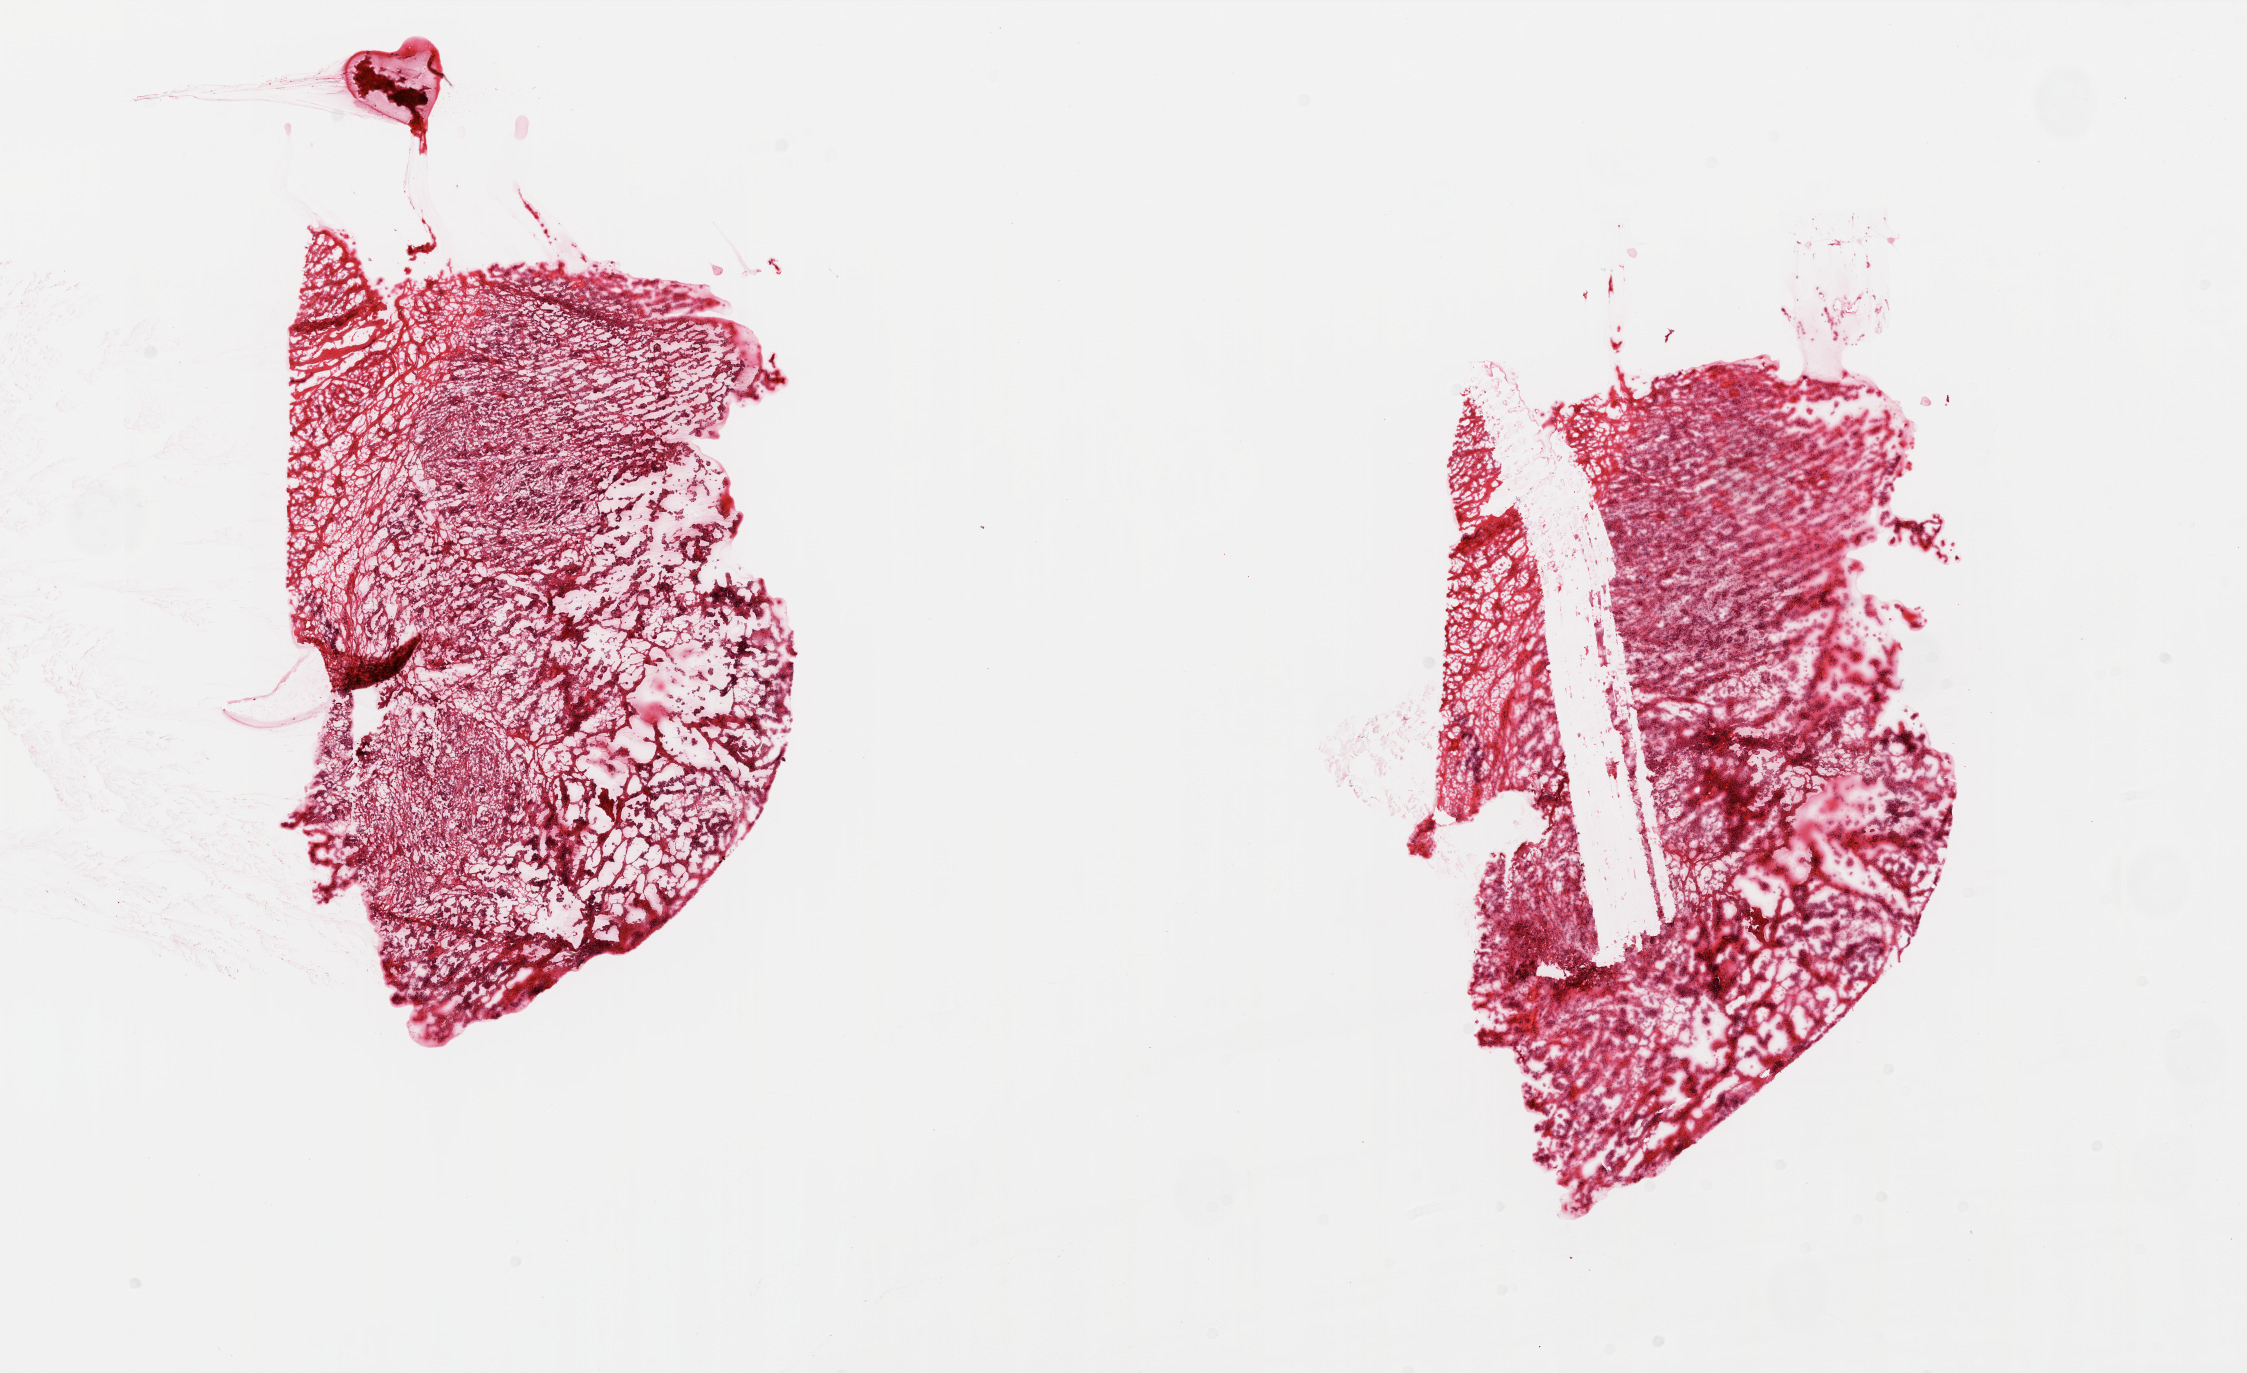
Hematoxylin and eosin (H&E) stained whole-slide image — whole scanned area (about 18.0 x 11.0 mm, acquisition: 20x scan) shown as a low-resolution overview, frozen section from the top of the tissue portion, ovary, primary tumour sample. Female patient; age at initial diagnosis 59 years. Histologic grade: G3 (poorly differentiated). Pathologist review of this section (percent, as recorded): tumour cells 90%, tumour nuclei 92%, normal cells 0%, stromal cells 10%, necrosis 0%.
• FIGO stage: IIIC
• pathologic diagnosis: Serous cystadenocarcinoma, NOS